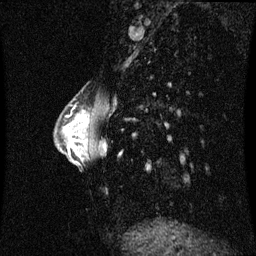
Breast MRI (dynamic contrast-enhanced), one sagittal slice; dynamic contrast-enhanced series, image 2 of 3 at this slice position (ordered by acquisition); 1.5 T; TE 4.2 ms, TR 8.9 ms; 256 × 256 image matrix, field of view 210 × 210 mm. Female patient, age 33 years. Case-level facts recorded for this patient, not image findings: setting: breast cancer imaged before/during neoadjuvant chemotherapy; receptor status: HER2-positive.
Structures marked on this image (semi-automatic segmentation, software-assisted and operator-edited):
- analysis volume of interest (the breast-tissue region the enhancement analysis was run in; not a lesion): bounding box (x1, y1, x2, y2) in pixels: (66, 111, 90, 141)
- tumour enhancement mask (voxels above the 70 % enhancement threshold inside the analysis volume of interest): (83, 117, 85, 119)